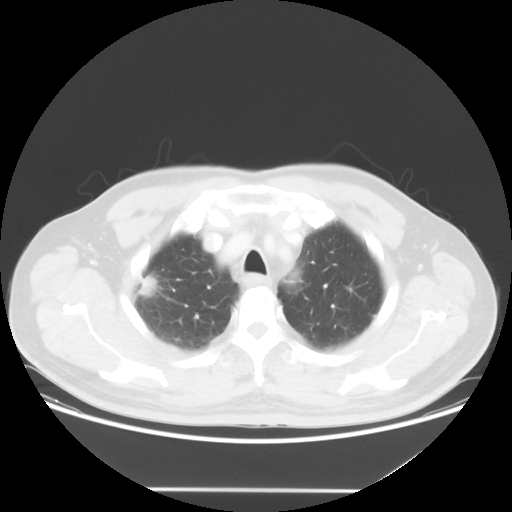
Chest CT, one axial slice; slice 44 of 54 in the series (ordered by position); reconstruction kernel STANDARD; 120 kVp; lung window (W 1500 / L -600 HU); 512 × 512 image matrix, field of view 416 × 416 mm. Male patient, age 65 years. From the clinical record (not read from this slice): clinical TNM (as recorded): T1c N1 M0.
Outlined on this slice (rectangle marked by the reading radiologist):
- lung tumour (recorded histology: adenocarcinoma): bounding box <133,268,163,302> (left, top, right, bottom; pixels)